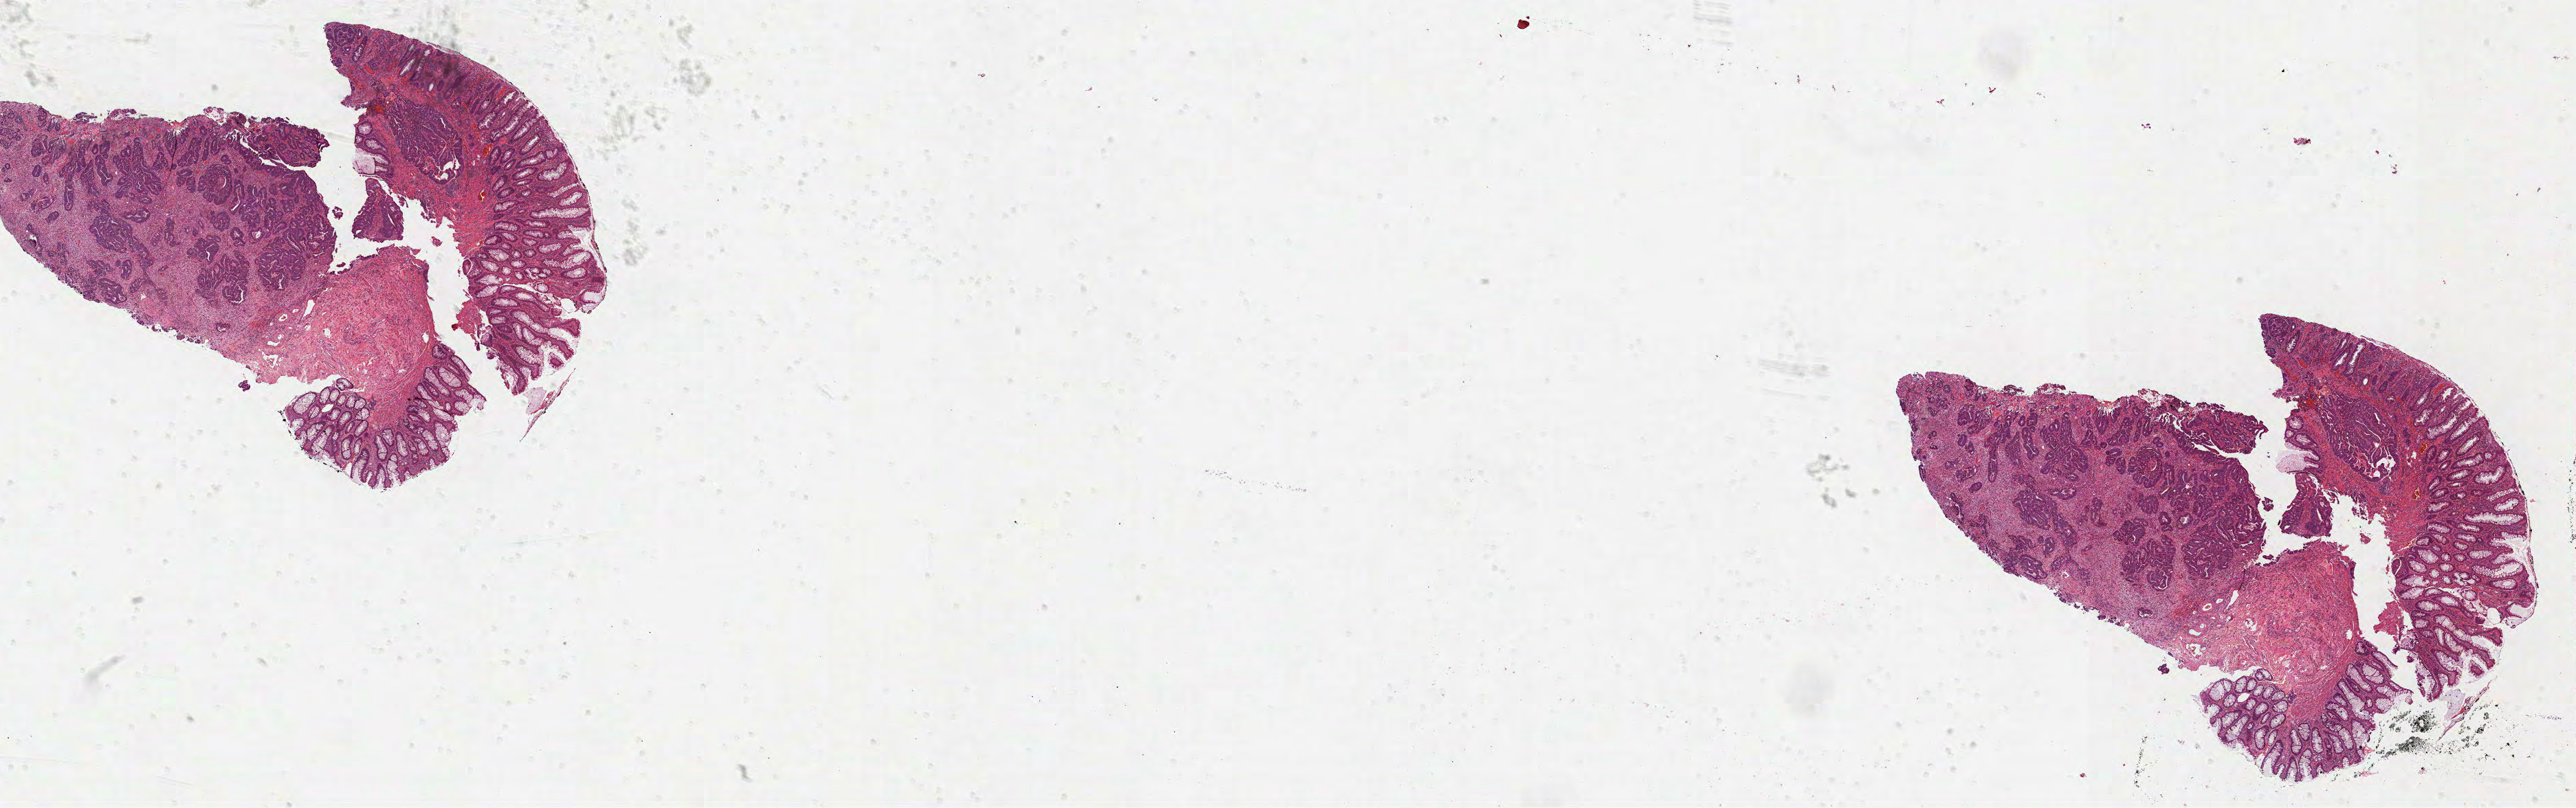
Digitized H&E-stained tissue section (whole slide), a low-resolution overview of the entire scanned area, about 30.2 x 9.5 mm (acquisition: 40x scan); formalin-fixed paraffin-embedded (FFPE) diagnostic section; rectum, primary tumour sample. Male, age 66 years at initial diagnosis.
AJCC pathologic stage: IIIA (7th edition). Histologic diagnosis: Adenocarcinoma, NOS (rectosigmoid junction). Lymph nodes positive (case pathology): 2 of 29 examined.